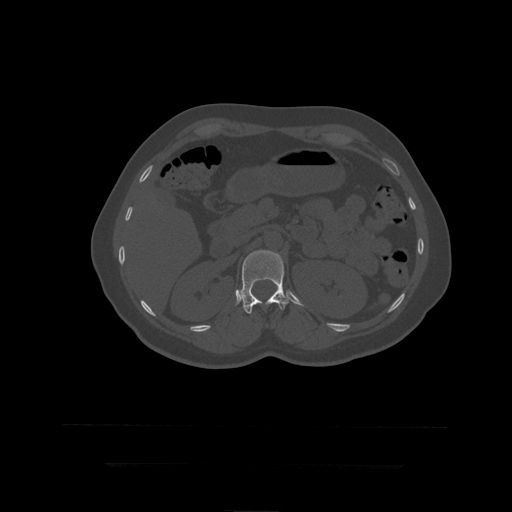
CT including the spine, one axial slice; 120 kVp; bone window (W 1800 / L 400 HU); 1.25 mm slice thickness; 512 × 512 image matrix, field of view 450 × 450 mm. Patient age 41 years. Case-level facts recorded for this patient, not image findings: primary cancer: breast.
Structures marked on this image (semi-automatic segmentation, software-assisted and operator-edited):
- L1 vertebra: box from (x=241, y=250) to (x=291, y=314) px